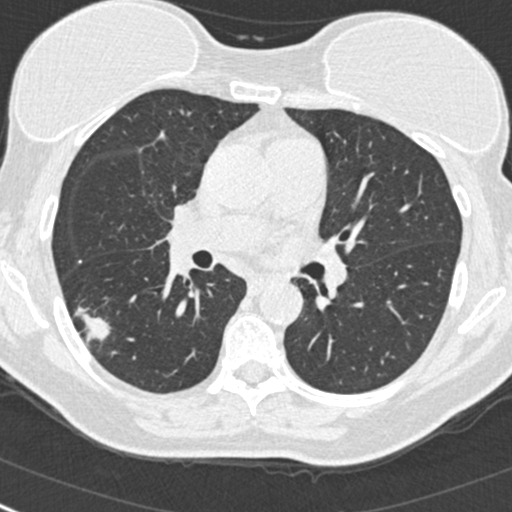
Low-dose screening chest CT, one axial slice. Slice 149 of 268 in the series (ordered by position). Lung window (W 1500 / L -600 HU). 512 × 512 image matrix, field of view 296 × 296 mm.
Structures marked on this image (expert manual segmentation):
- lesion 1 (tumor, upper lobe of right lung): bounding box (x1, y1, x2, y2) in pixels: (74, 307, 110, 341)